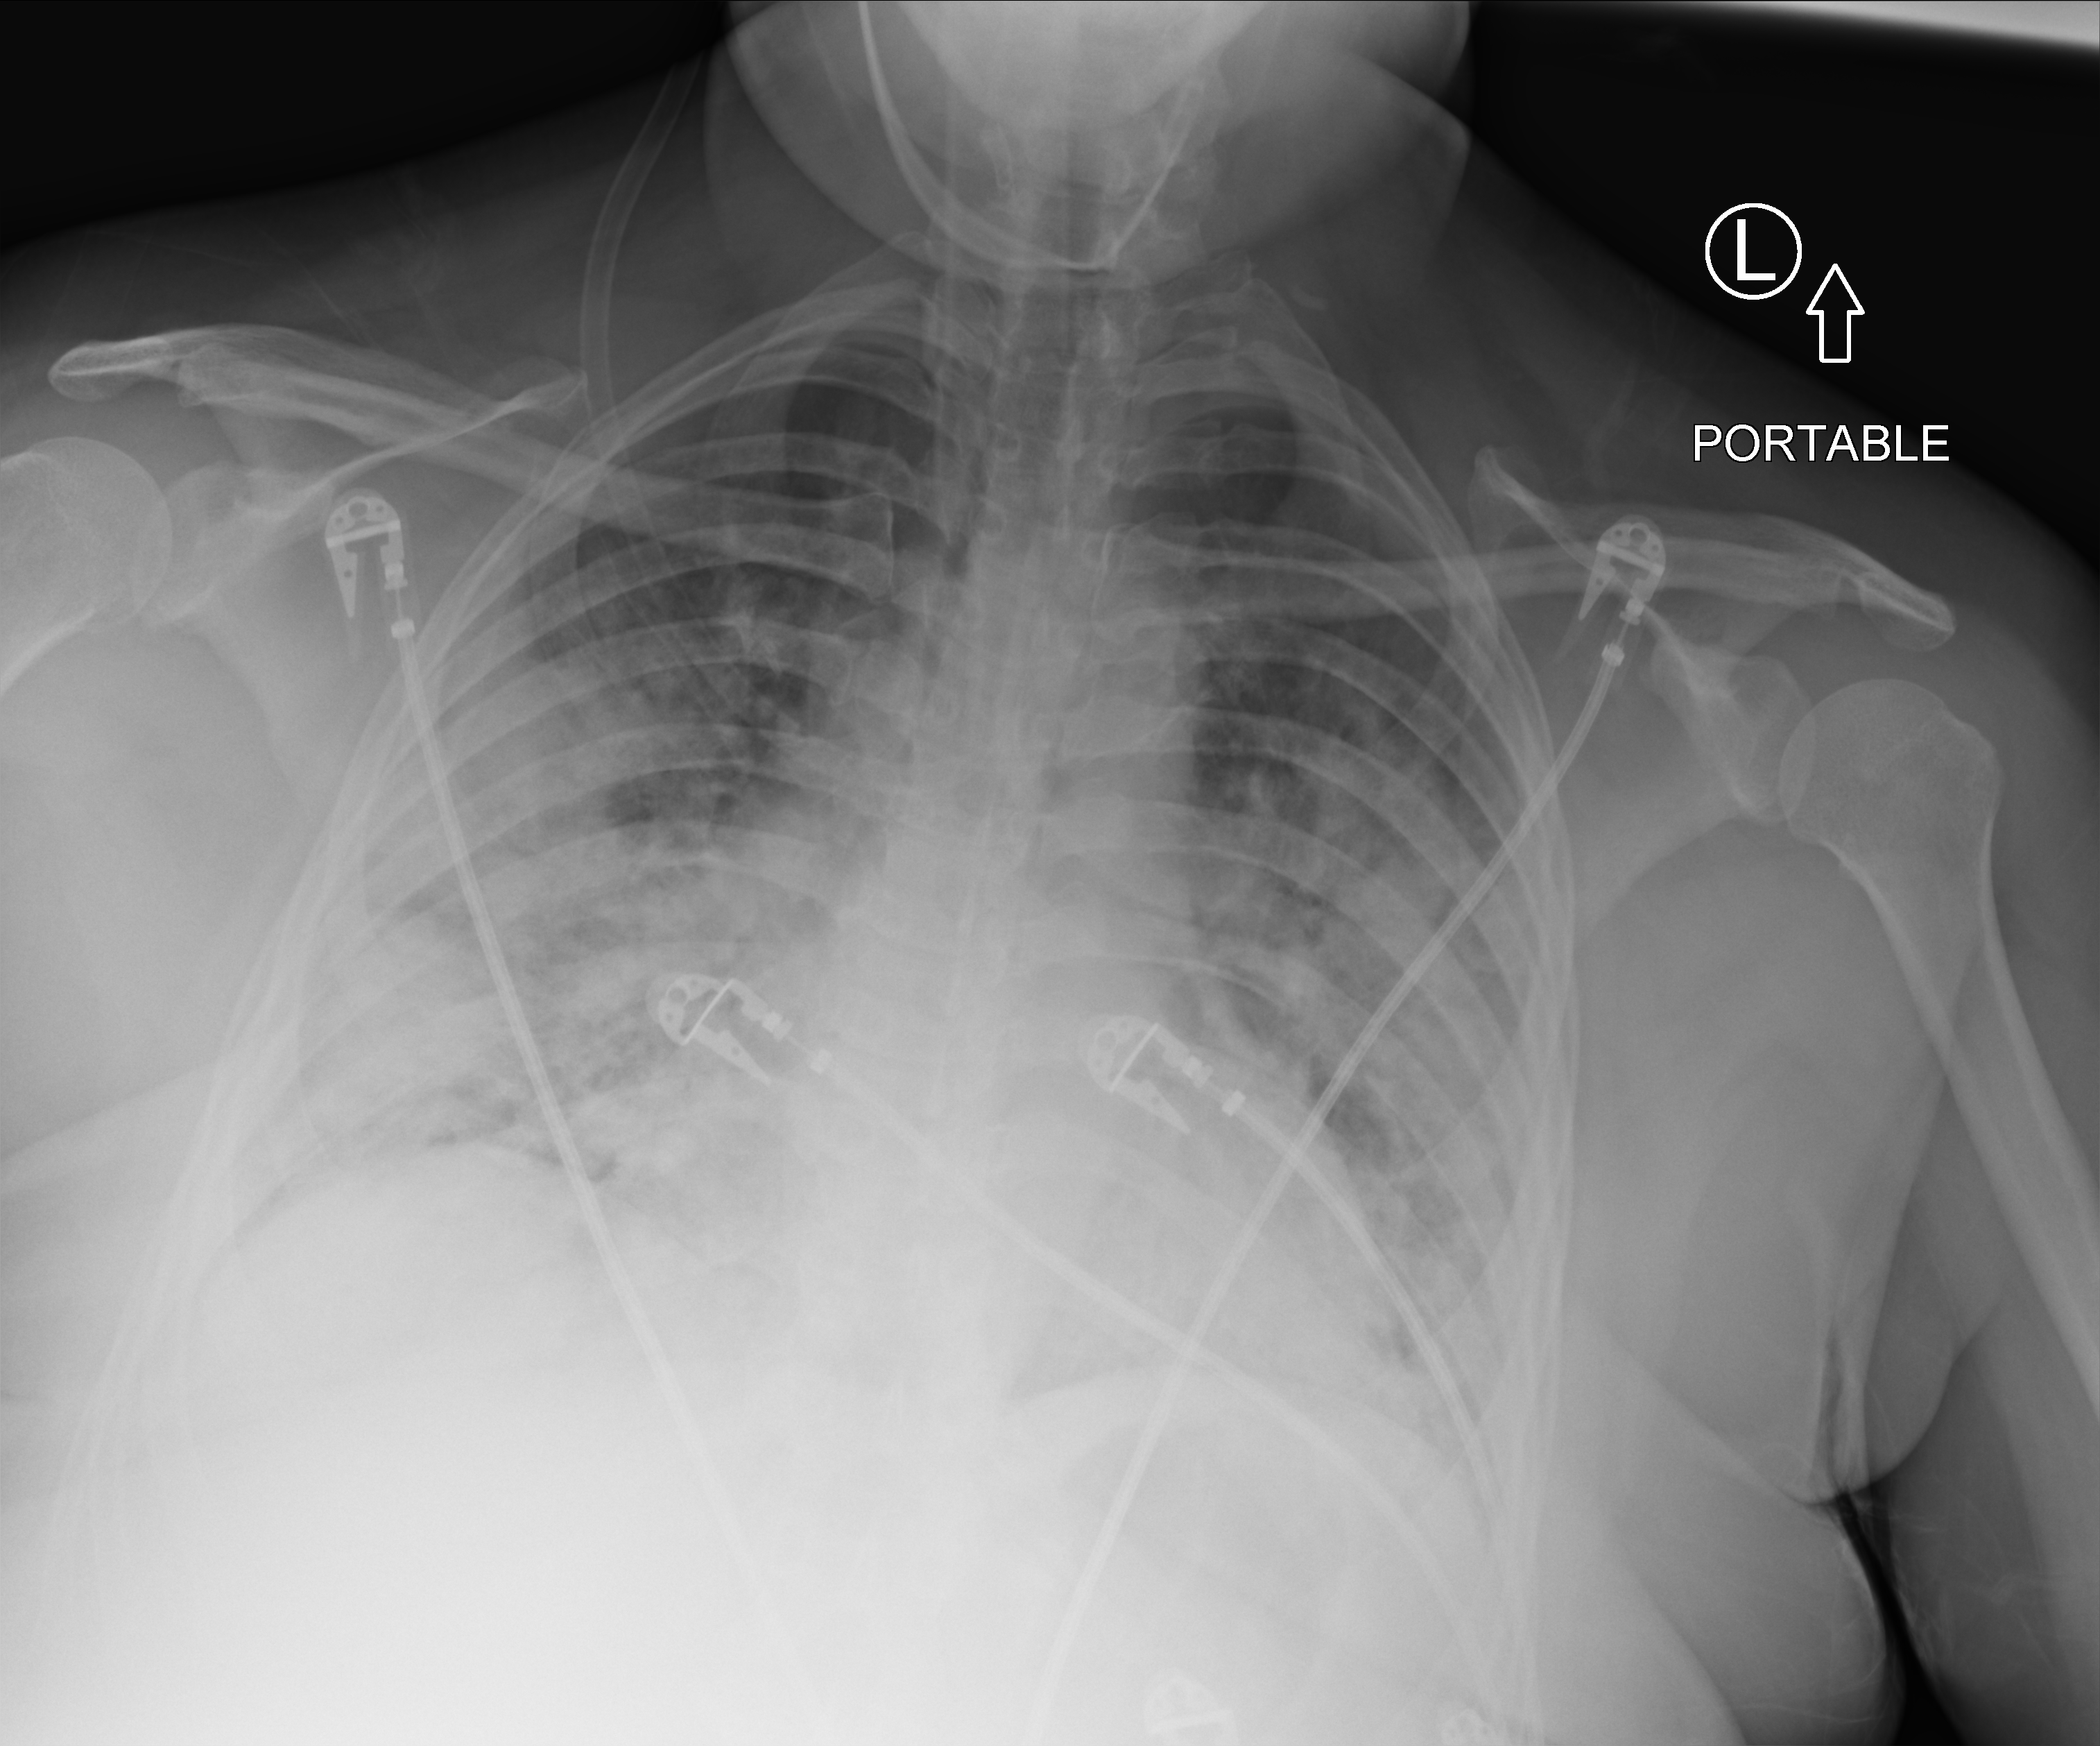
Portable chest radiograph, anteroposterior (AP) projection. Patient hospitalised with COVID-19; female, aged 18–59 years.
From the hospital-stay record, not from the radiograph (when in the stay this image was taken is not recorded): mechanically ventilated during this hospital stay: no.